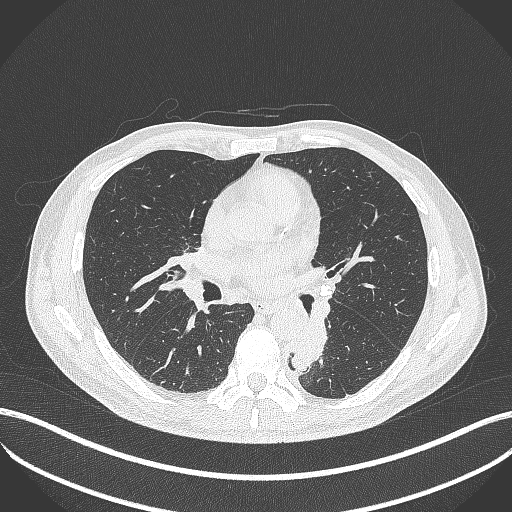
Chest CT, one axial slice; slice 216 of 451 in the series (ordered by position); reconstruction kernel B70f; lung window (W 1500 / L -600 HU); 512 × 512 image matrix, field of view 400 × 400 mm. Patient: male, 72 years. Case-level facts recorded for this patient, not image findings: clinical TNM (as recorded): T2b N0 M1.
Structures marked on this image (bounding box drawn by a radiologist):
- lung tumour (recorded histology: adenocarcinoma): bounding box <286,317,336,375> (left, top, right, bottom; pixels)